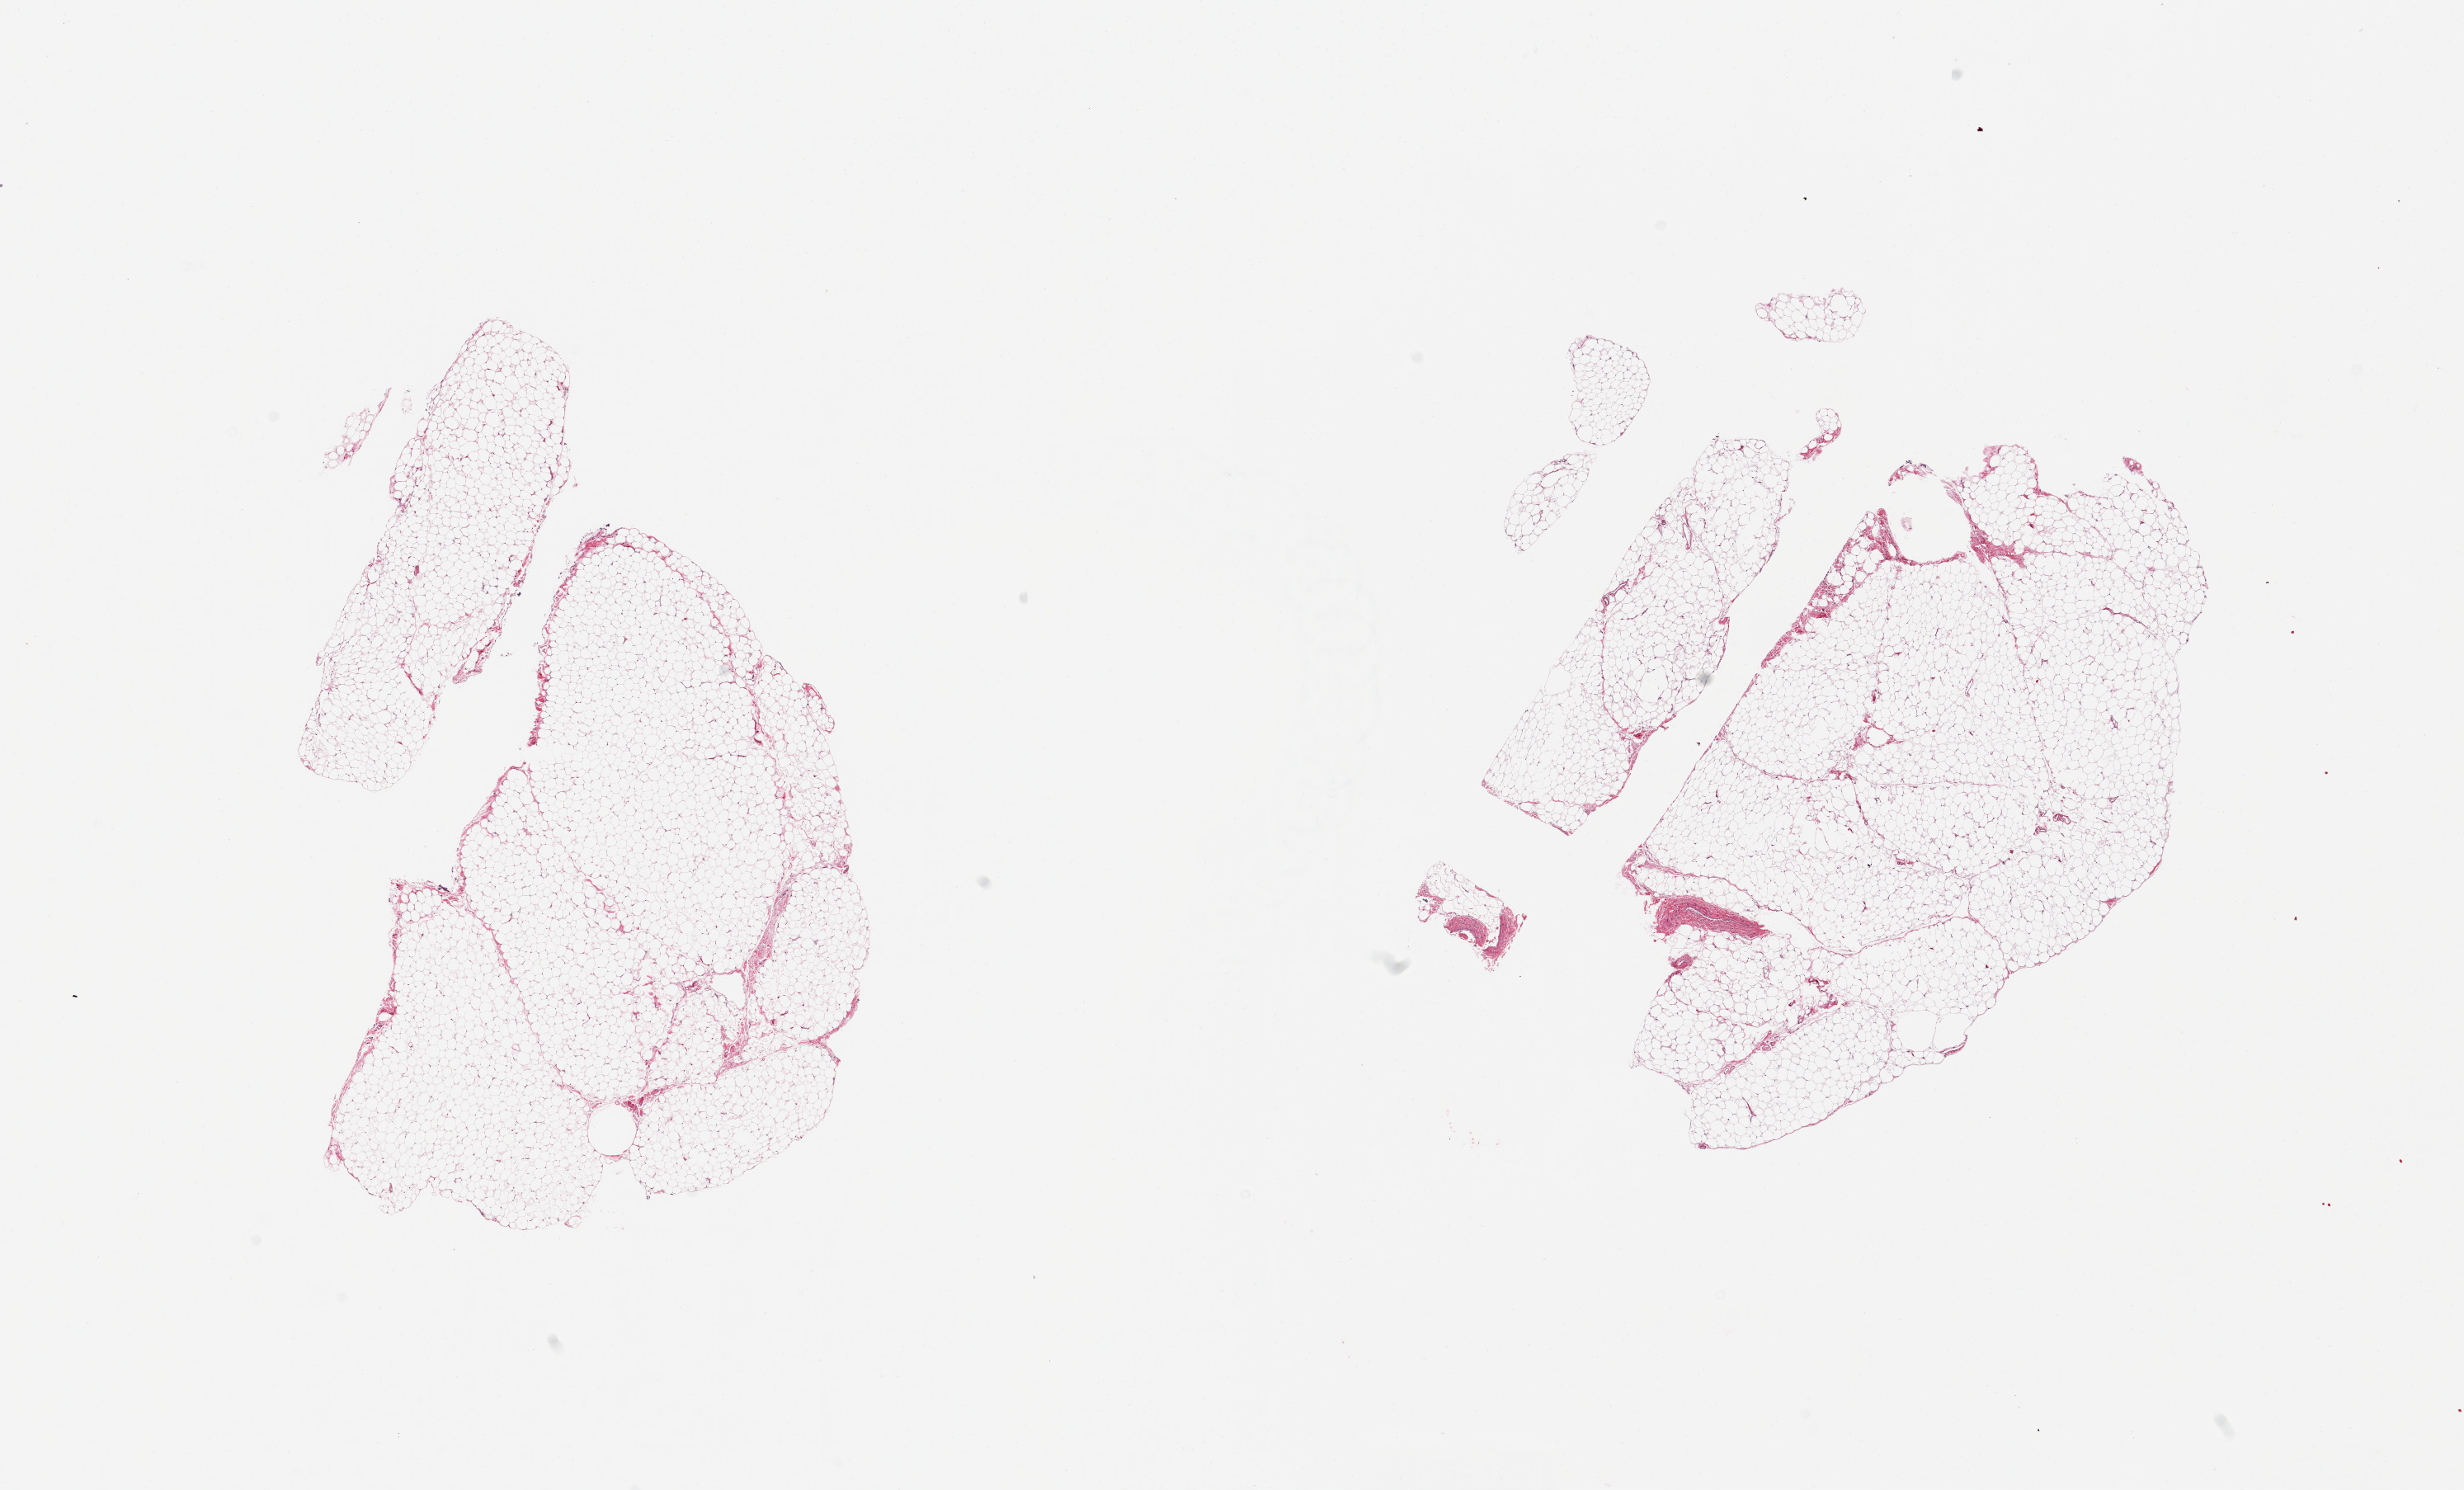
Whole-slide image, hematoxylin and eosin (H&E) stain, a low-resolution overview of the entire scanned area, about 23.6 x 14.3 mm; PAXgene-fixed paraffin-embedded (PFPE) section; section of omentum (target tissue); tissue donor sample. Donor: female.
* reviewer comment on this tissue sample: 2 pieces